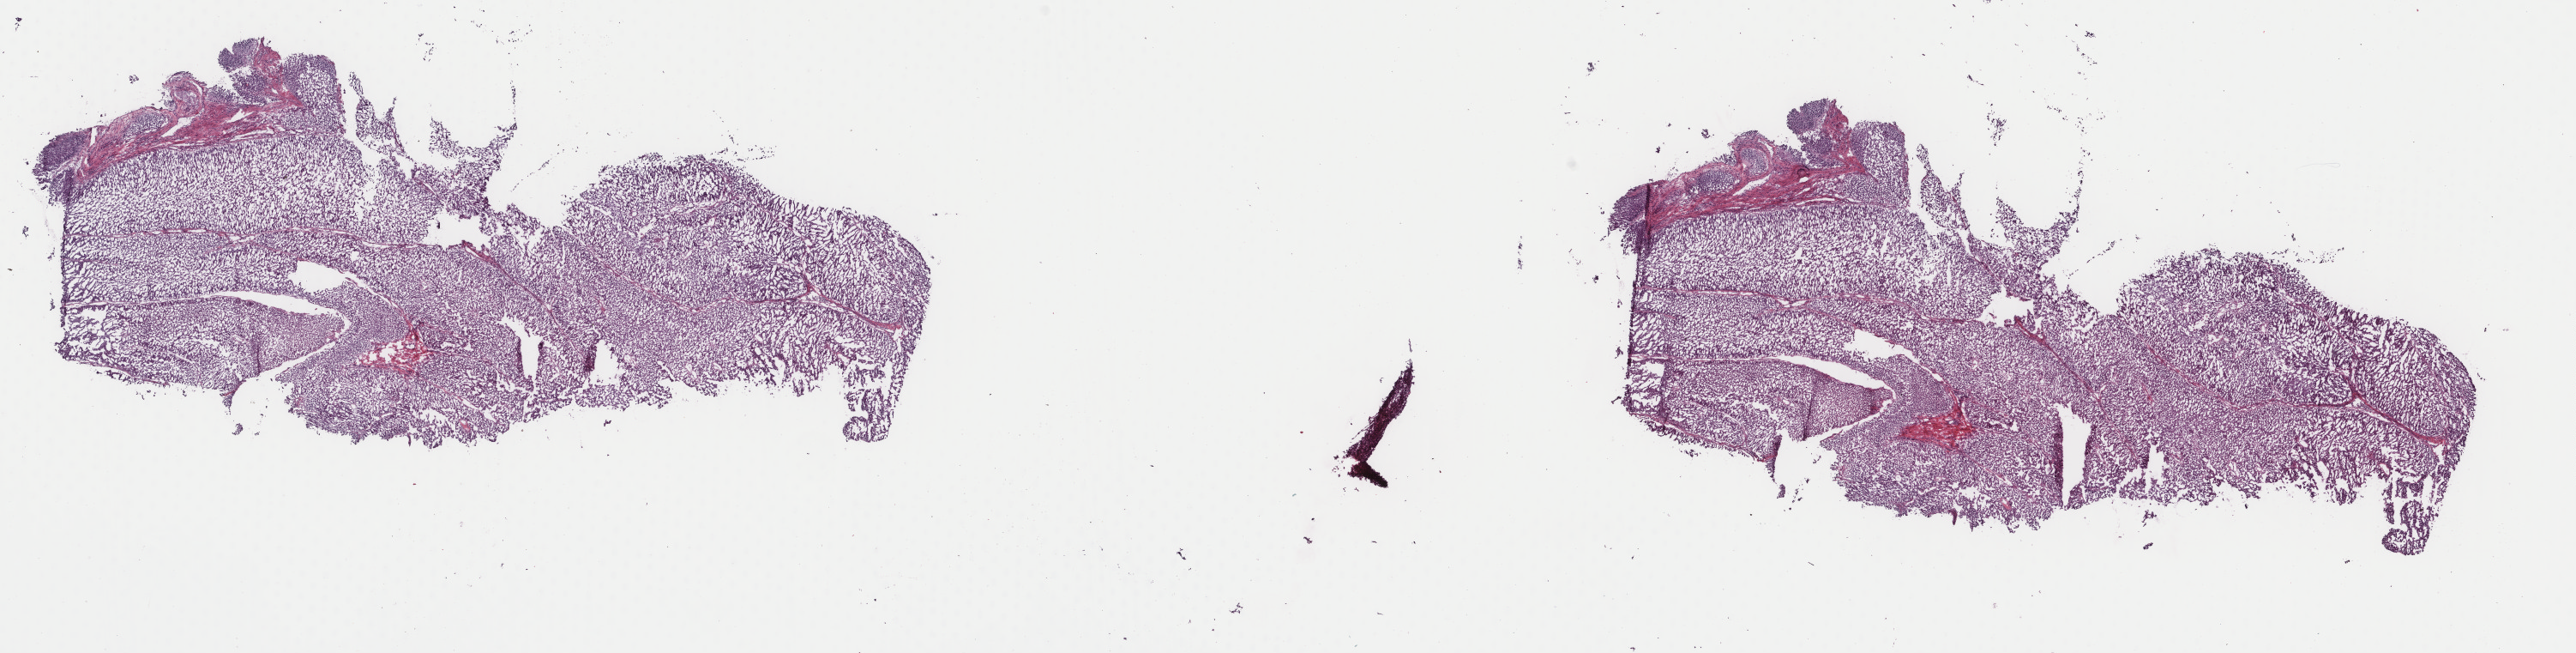
Whole-slide histology image, H&E-stained — low-resolution overview of the scanned area, about 23.8 x 6.0 mm (slide scanned at 40x); frozen section from the top of the tissue portion; primary tumour sample from the bladder. Male, age 55 years at initial diagnosis. Histologic grade: low grade. Composition of this section per pathologist review: tumour cells 95%, tumour nuclei 99%, normal cells 0%, stromal cells 5%, necrosis 0%. Infiltration values recorded for this section: lymphocyte infiltration 0%, monocyte infiltration 0%, neutrophil infiltration 0%.
Diagnosis: Papillary transitional cell carcinoma. AJCC pathologic stage: II (7th edition).